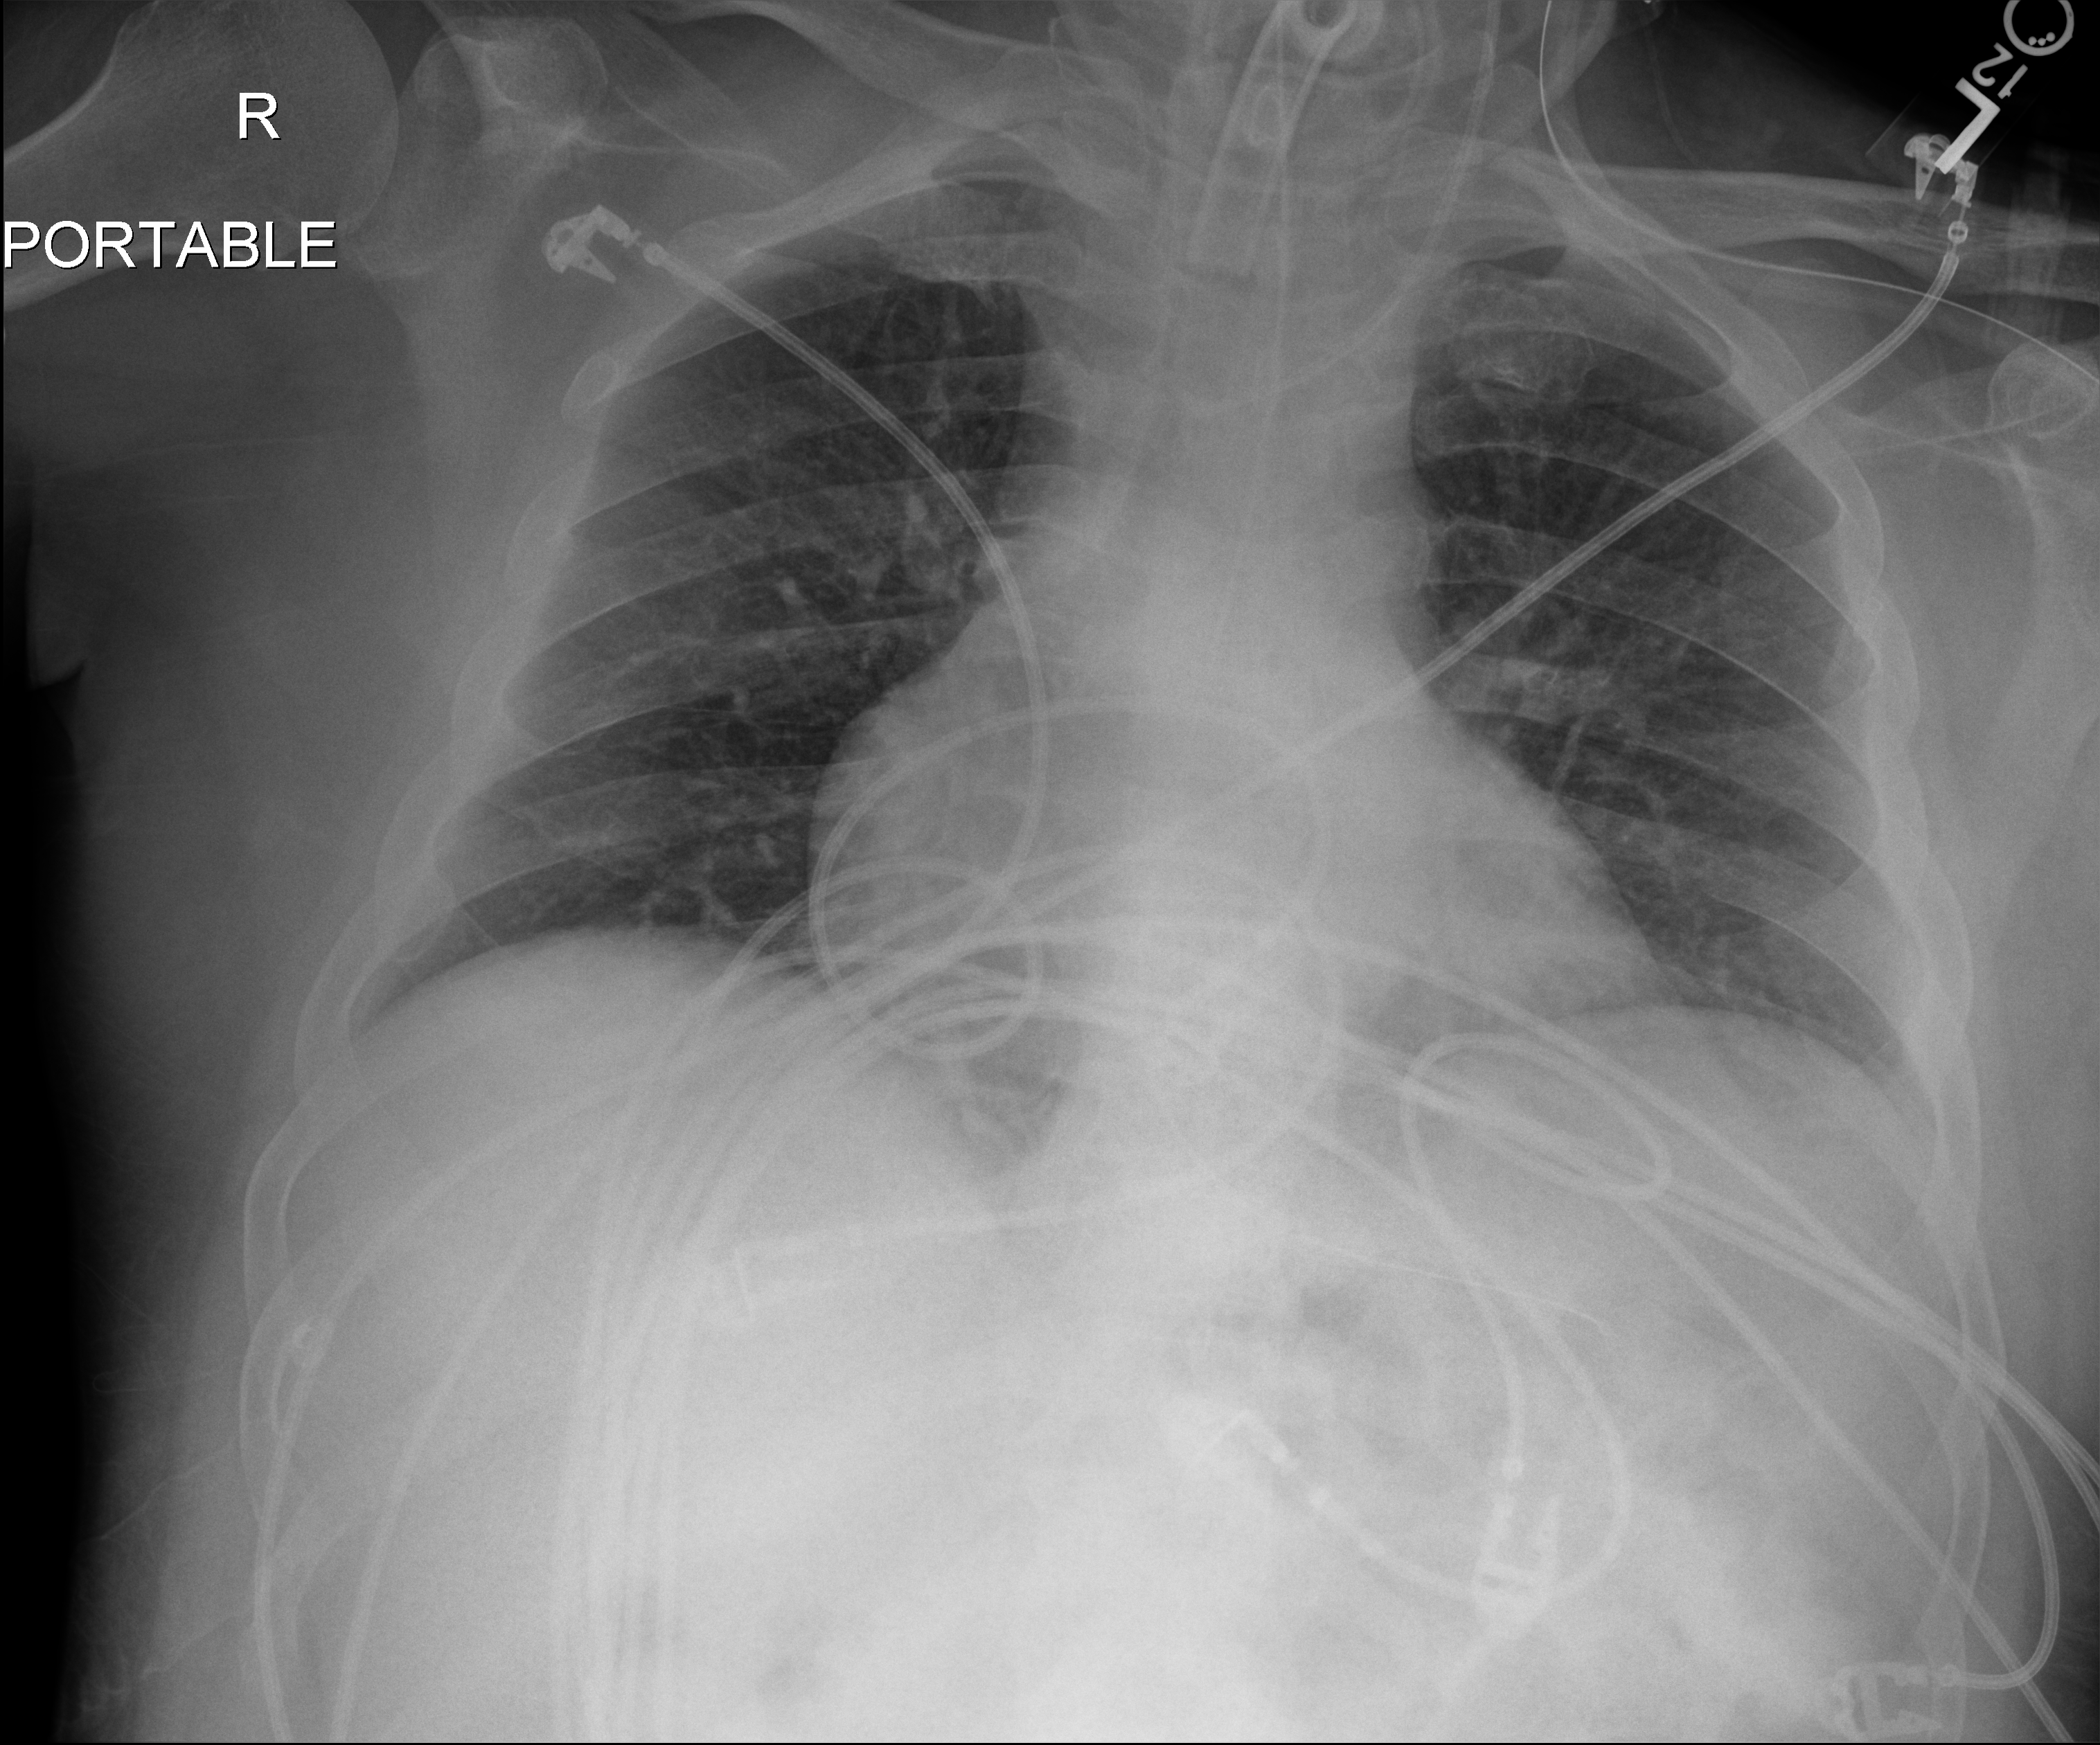
Chest X-ray (portable). Patient hospitalised with COVID-19; male, aged 18–59 years.
Admission-level facts for this patient (not findings on this image; timing relative to this image not recorded):
- admitted to intensive care during this hospital stay: yes
- mechanically ventilated during this hospital stay: yes